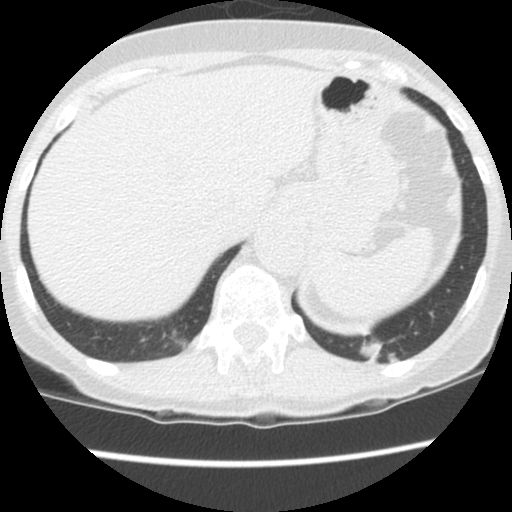
Low-dose screening chest CT, one axial slice. Position 22 of 130 along the scan axis. 120 kVp. Lung window (W 1500 / L -600 HU). 2.5 mm slice thickness. 512 × 512 image matrix, field of view 290 × 290 mm.
Outlined on this slice (outlined manually by an expert reader):
- lesion 1 (tumor, lower lobe of left lung): bounding box (x1, y1, x2, y2) in pixels: (359, 338, 383, 364)